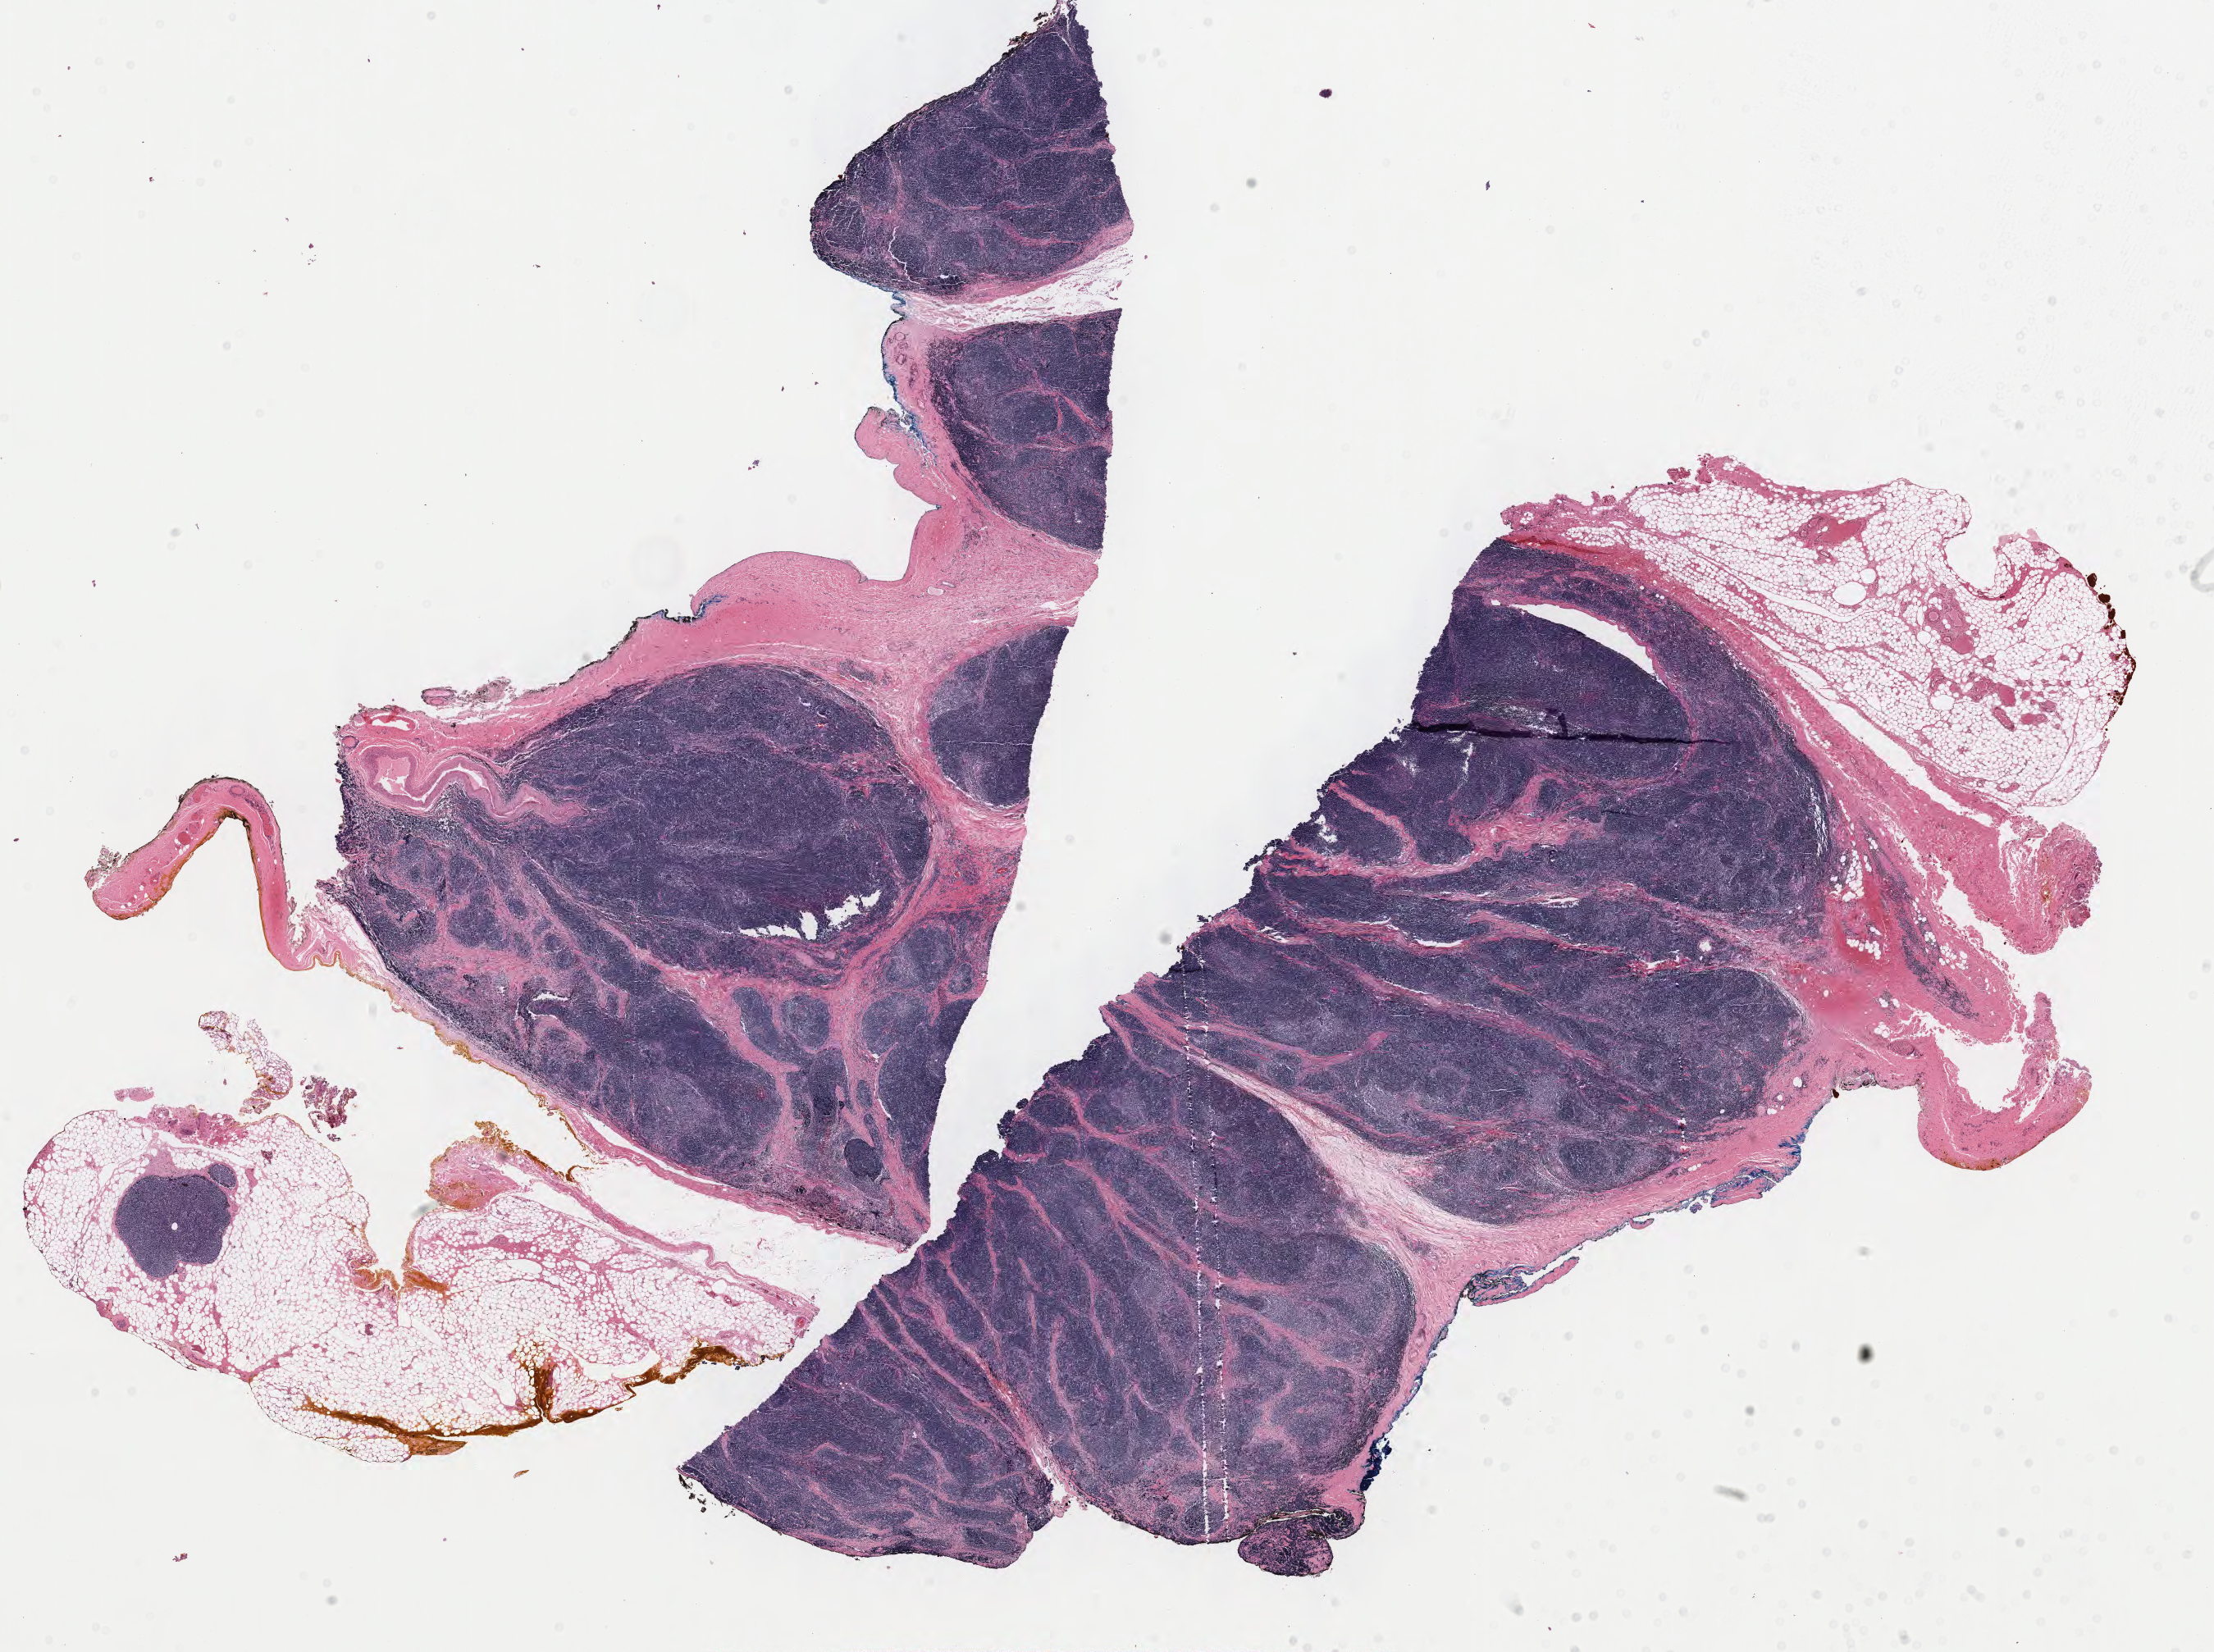
Hematoxylin and eosin (H&E) stained whole-slide image, low-resolution overview of the scanned area, about 21.4 x 16.0 mm. Formalin-fixed paraffin-embedded (FFPE) diagnostic section. Sample: primary tumour, thymus. Female patient; age at initial diagnosis 57 years.
Pathologic diagnosis: Thymoma, type B1, NOS.